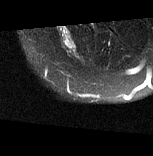
MRI of an extremity soft-tissue mass, one axial slice. Slice 13 of 77 in the series (ordered by position). T2-weighted fat-saturated. MR volume resampled by the dataset authors to the PET/CT grid (not the native acquisition matrix). 3.27 mm slice thickness. 153 × 156 image matrix, field of view 149 × 152 mm. Female patient. Case-level facts recorded for this patient, not image findings: histological type: synovial sarcoma; grade: intermediate; site of the primary tumour: right buttock.
Structures marked on this image (expert contour drawn on MRI and transferred to this co-registered scan by the dataset authors):
- gross tumour volume including surrounding oedema: bounding box [x1, y1, x2, y2] px = [58, 27, 77, 55]